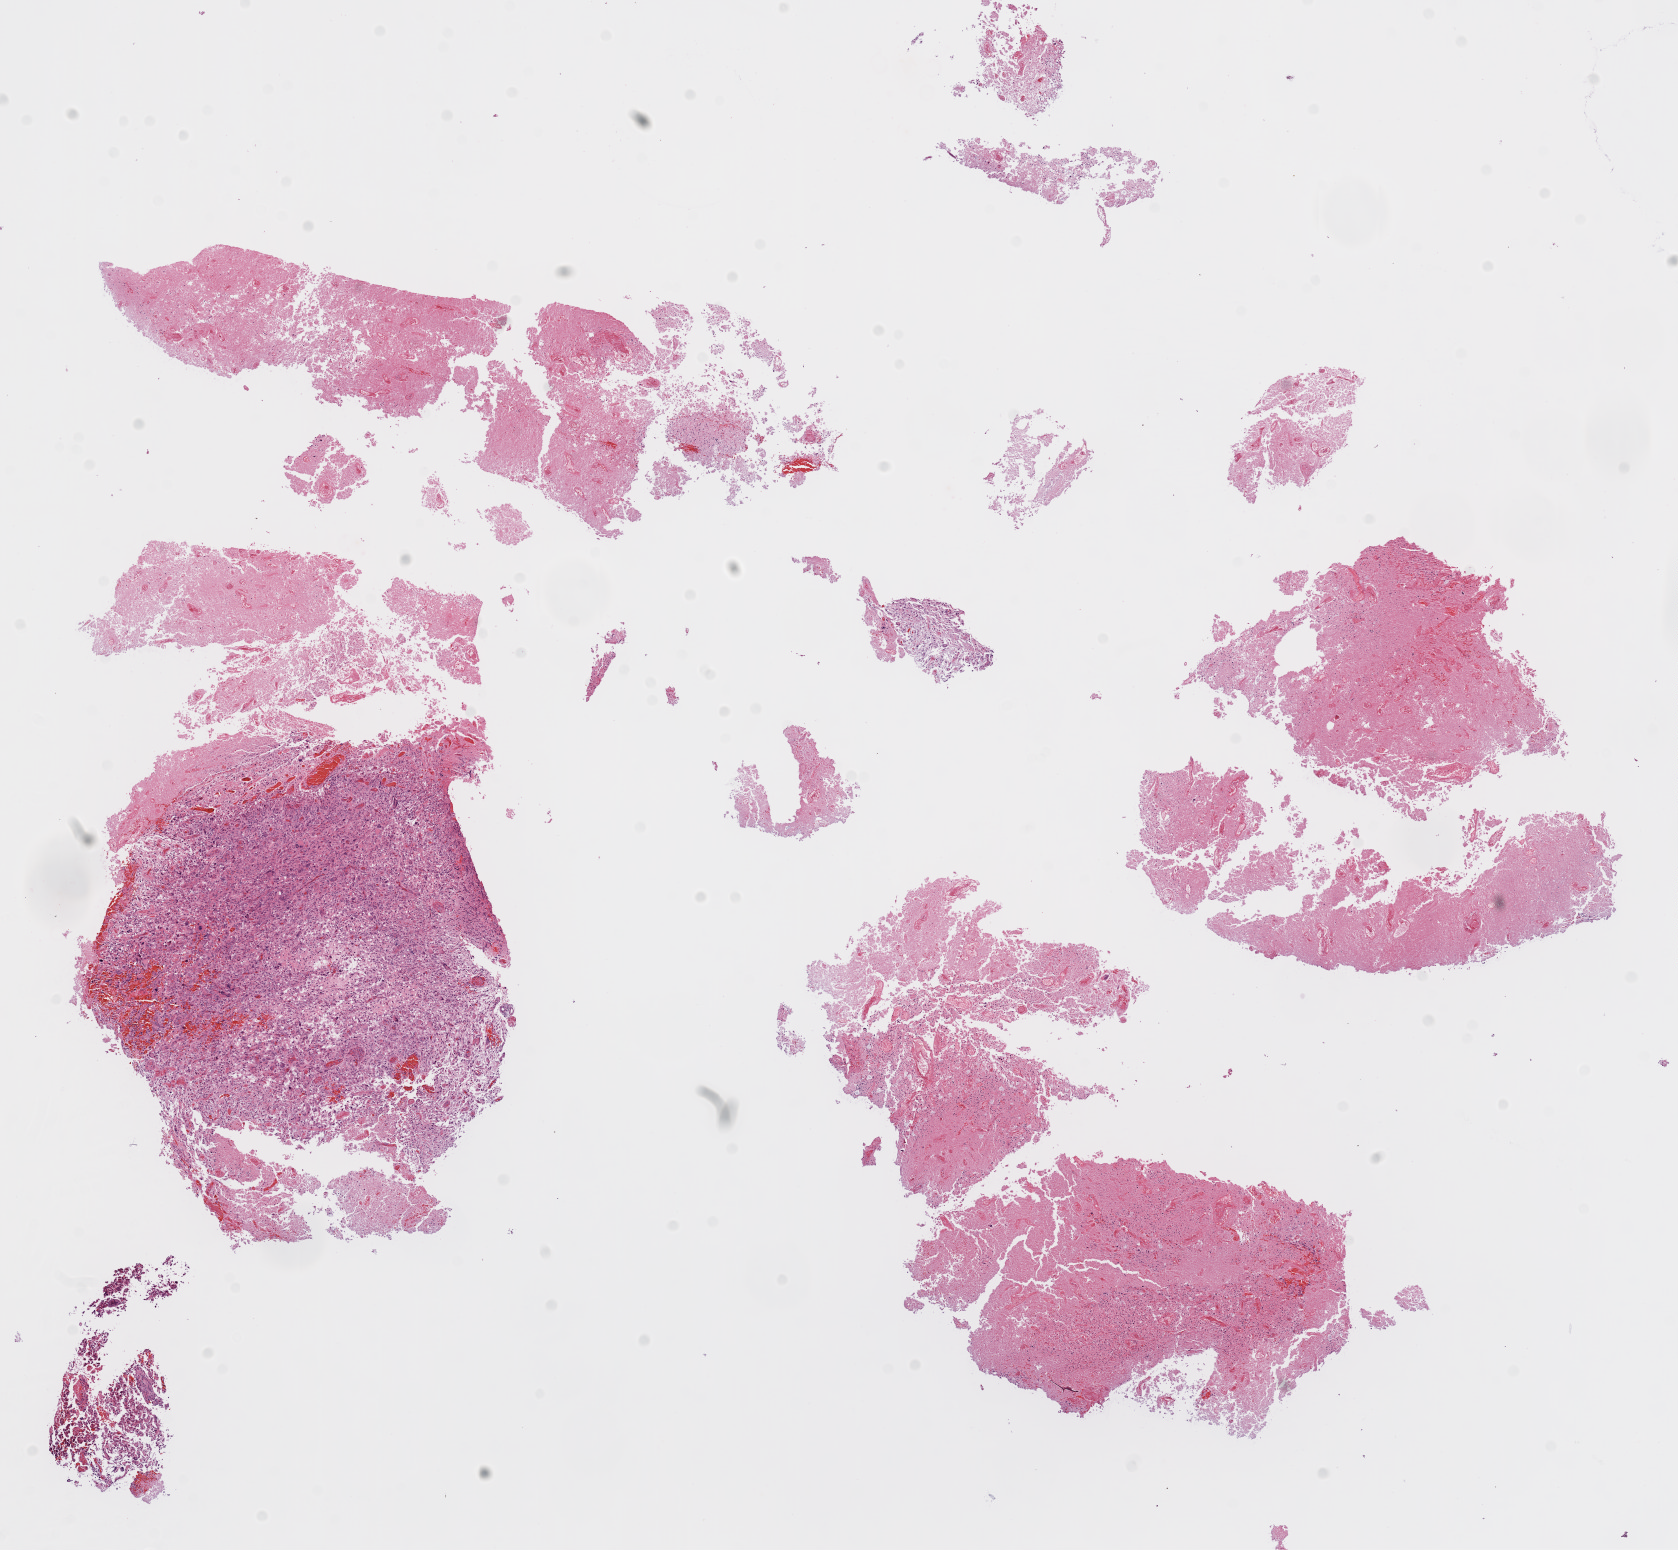
Whole-slide histology image, Hematoxylin and eosin (H&E) stained, a low-resolution overview of the entire scanned area, about 13.5 x 12.5 mm (slide scanned at 20x), formalin-fixed paraffin-embedded (FFPE) diagnostic section, brain, primary tumour sample. Female patient; age at initial diagnosis 55 years.
Diagnosis: Glioblastoma.